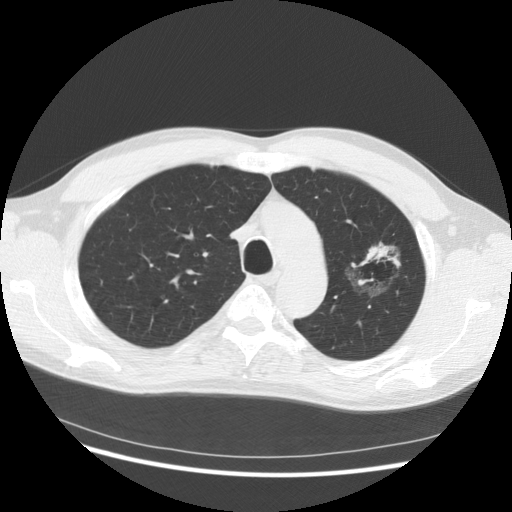
Low-dose screening chest CT, one axial slice. Position 106 of 145 along the scan axis. Lung window (W 1500 / L -600 HU). 2.5 mm slice thickness. 512 × 512 image matrix.
Annotated regions visible in this slice (outlined manually by an expert reader):
- lesion 1 (tumor, upper lobe of left lung): bounding box [x1, y1, x2, y2] px = [363, 244, 395, 264]